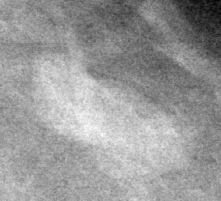
Region of interest cut from a scanned film mammogram (one marked finding), left breast, CC view.
Finding: mass, shape lymph node, margins circumscribed; BI-RADS assessment category 3; subtlety rating 2 on a 1 (subtle) to 5 (obvious) scale; benign without callback (not worked up further).